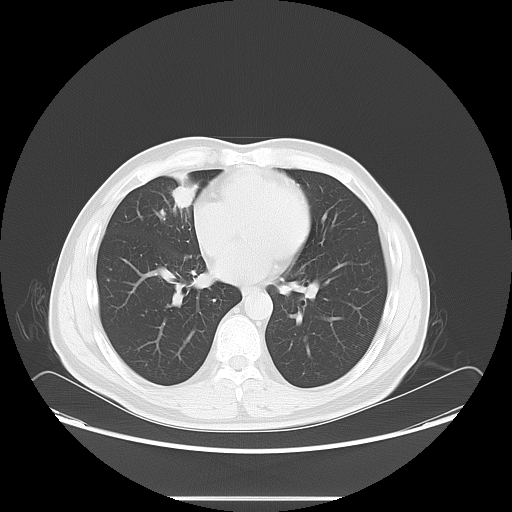
Chest CT, one axial slice. Slice 35 of 73 in the series (ordered by position). Lung window (W 1500 / L -600 HU). 5 mm slice thickness. 512 × 512 image matrix, field of view 429 × 429 mm. Male patient, age 47 years. From the clinical record (not read from this slice): clinical TNM (as recorded): T1c N3 M0.
Outlined on this slice (rectangle marked by the reading radiologist):
- lung tumour (recorded histology: adenocarcinoma): bounding box (x1, y1, x2, y2) in pixels: (164, 182, 210, 212)